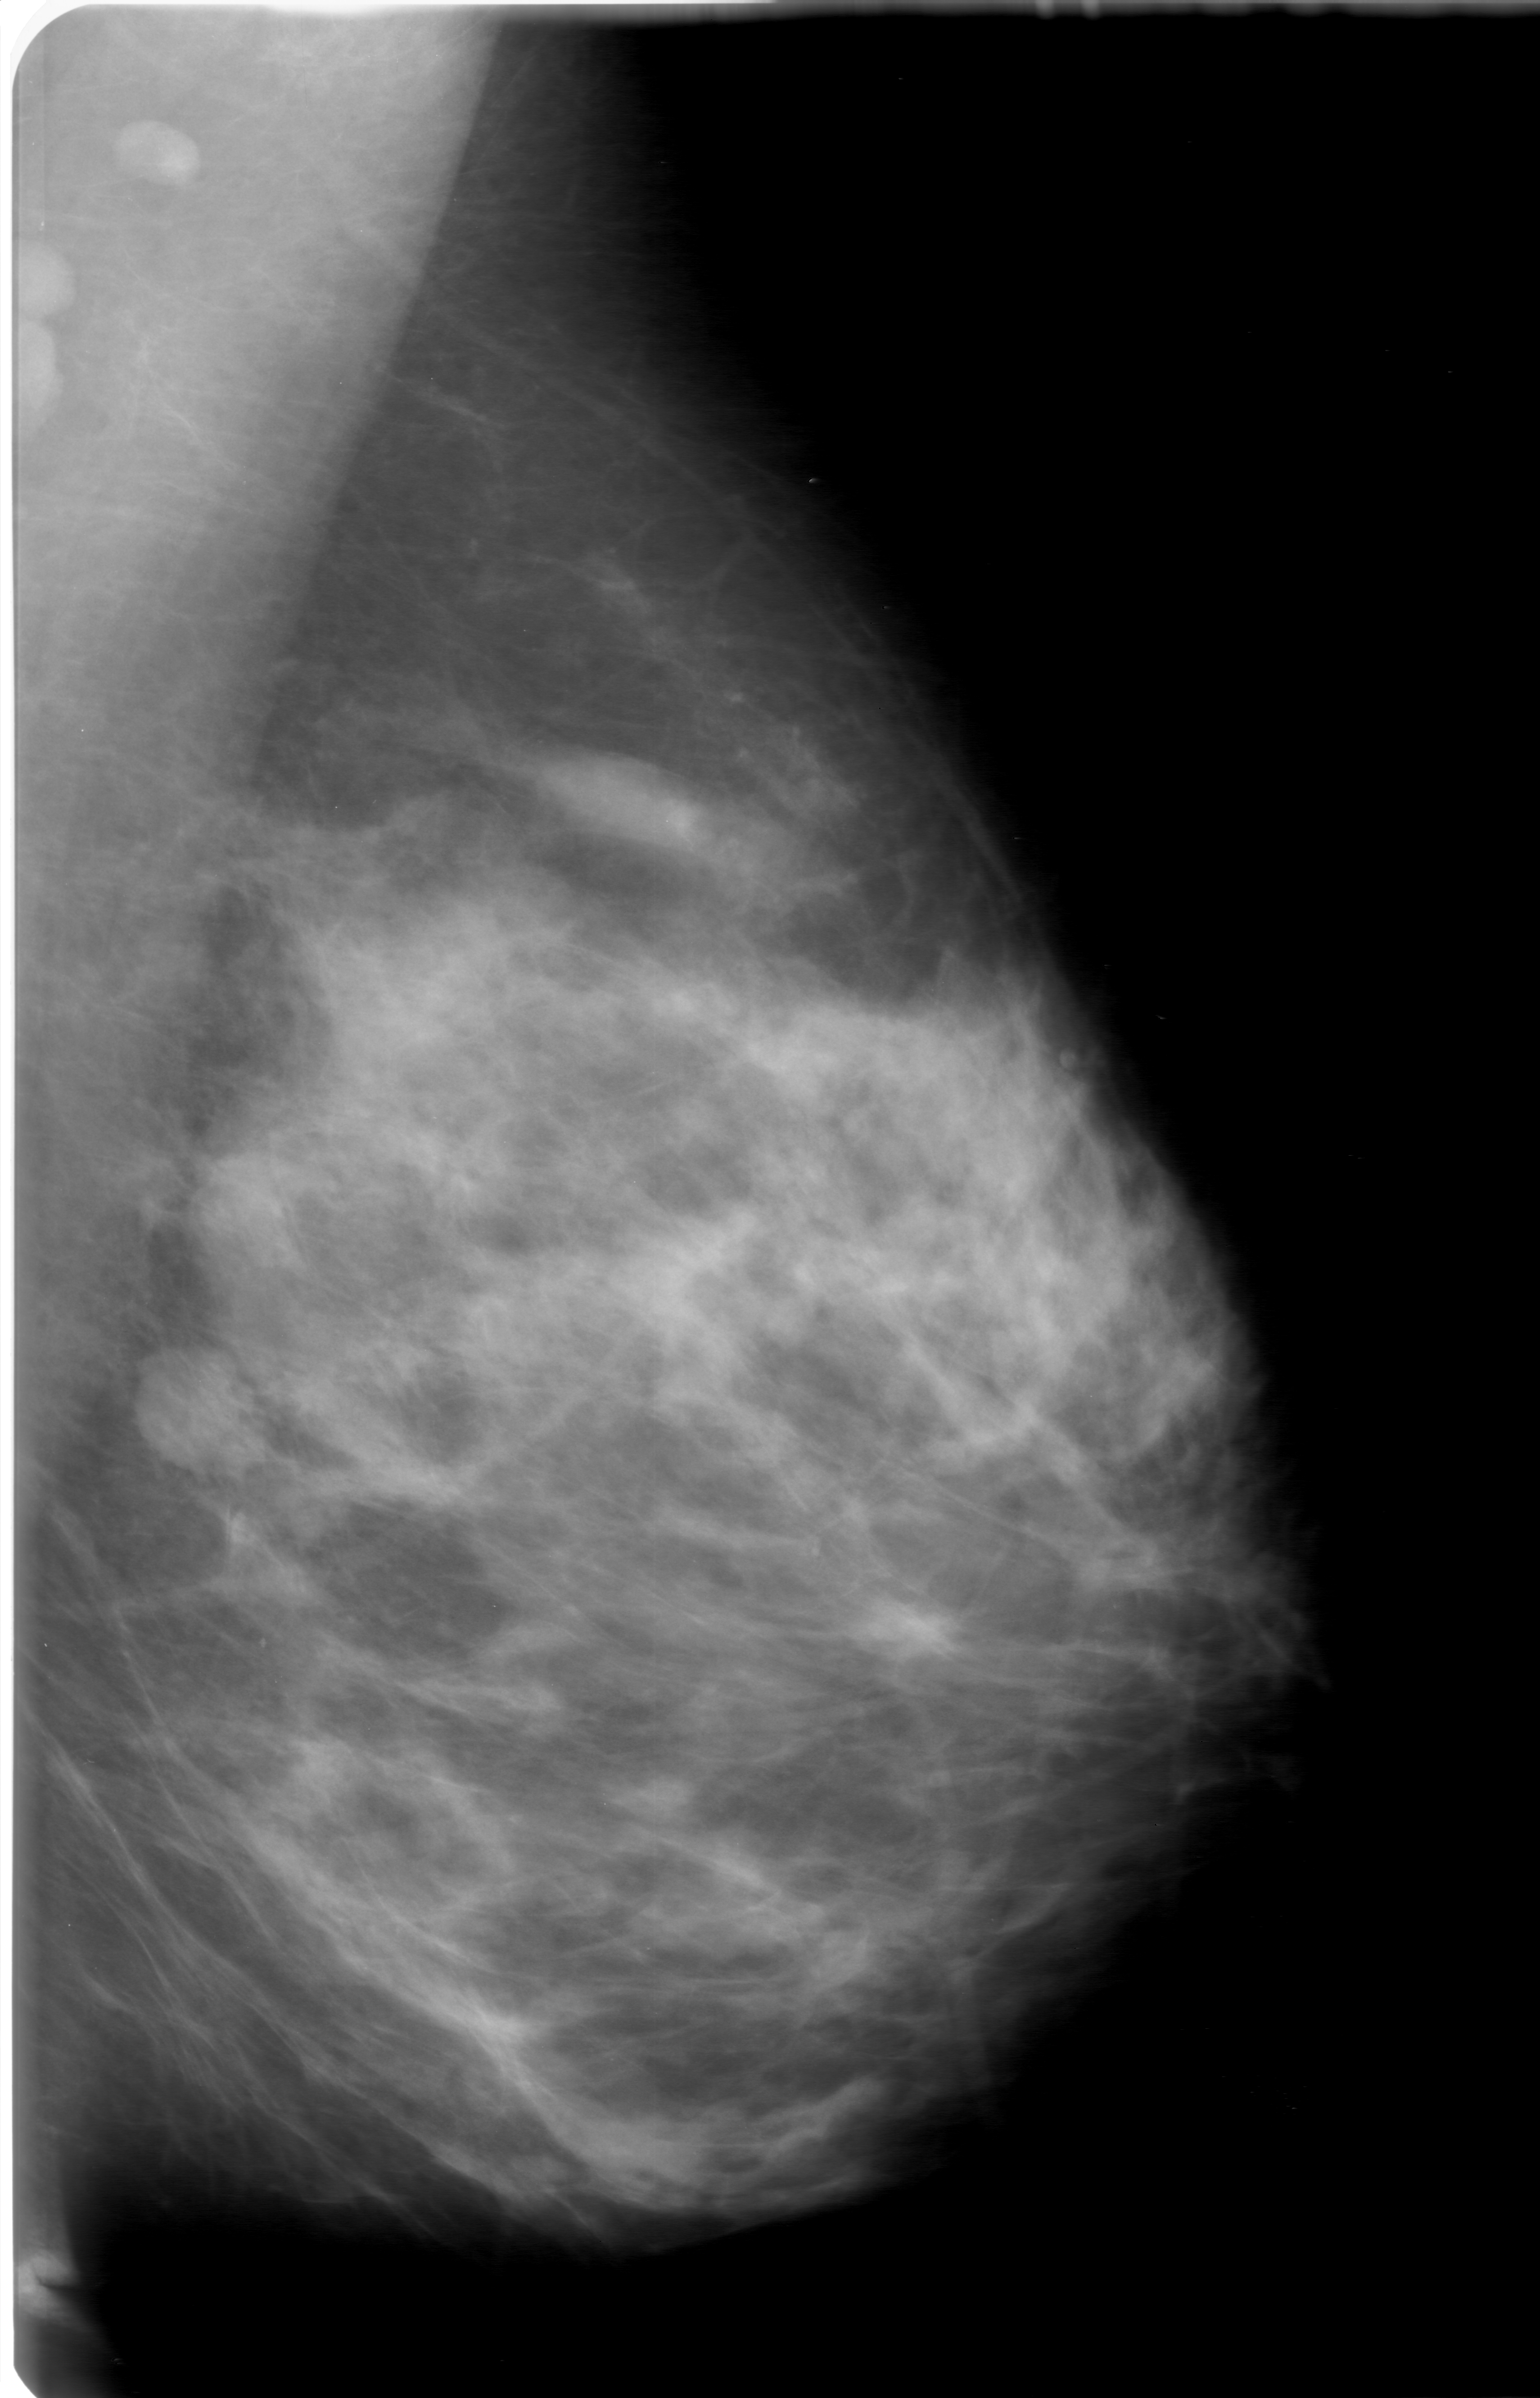
Mammogram (digitized film); left breast; MLO view.
Marked findings (only marked abnormalities are described; nothing is implied about the rest of the image): mass, shape lobulated, margins microlobulated; BI-RADS assessment category 3; pathology result (as recorded, not read from the image): benign.